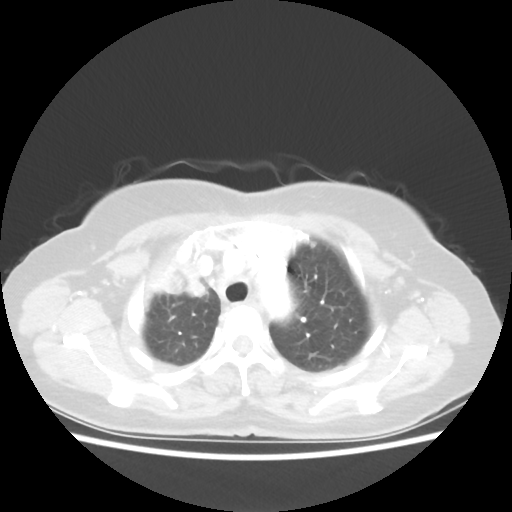
Chest CT, one axial slice; position 43 of 55 along the scan axis; lung window (W 1500 / L -600 HU); 5 mm slice thickness; 512 × 512 image matrix, field of view 337 × 337 mm. Female patient, age 62 years. From the clinical record (not read from this slice): clinical TNM (as recorded): T4 N3 M0.
Outlined on this slice (rectangle marked by the reading radiologist):
- lung tumour (recorded histology: squamous cell carcinoma): box from (x=149, y=247) to (x=205, y=312) px